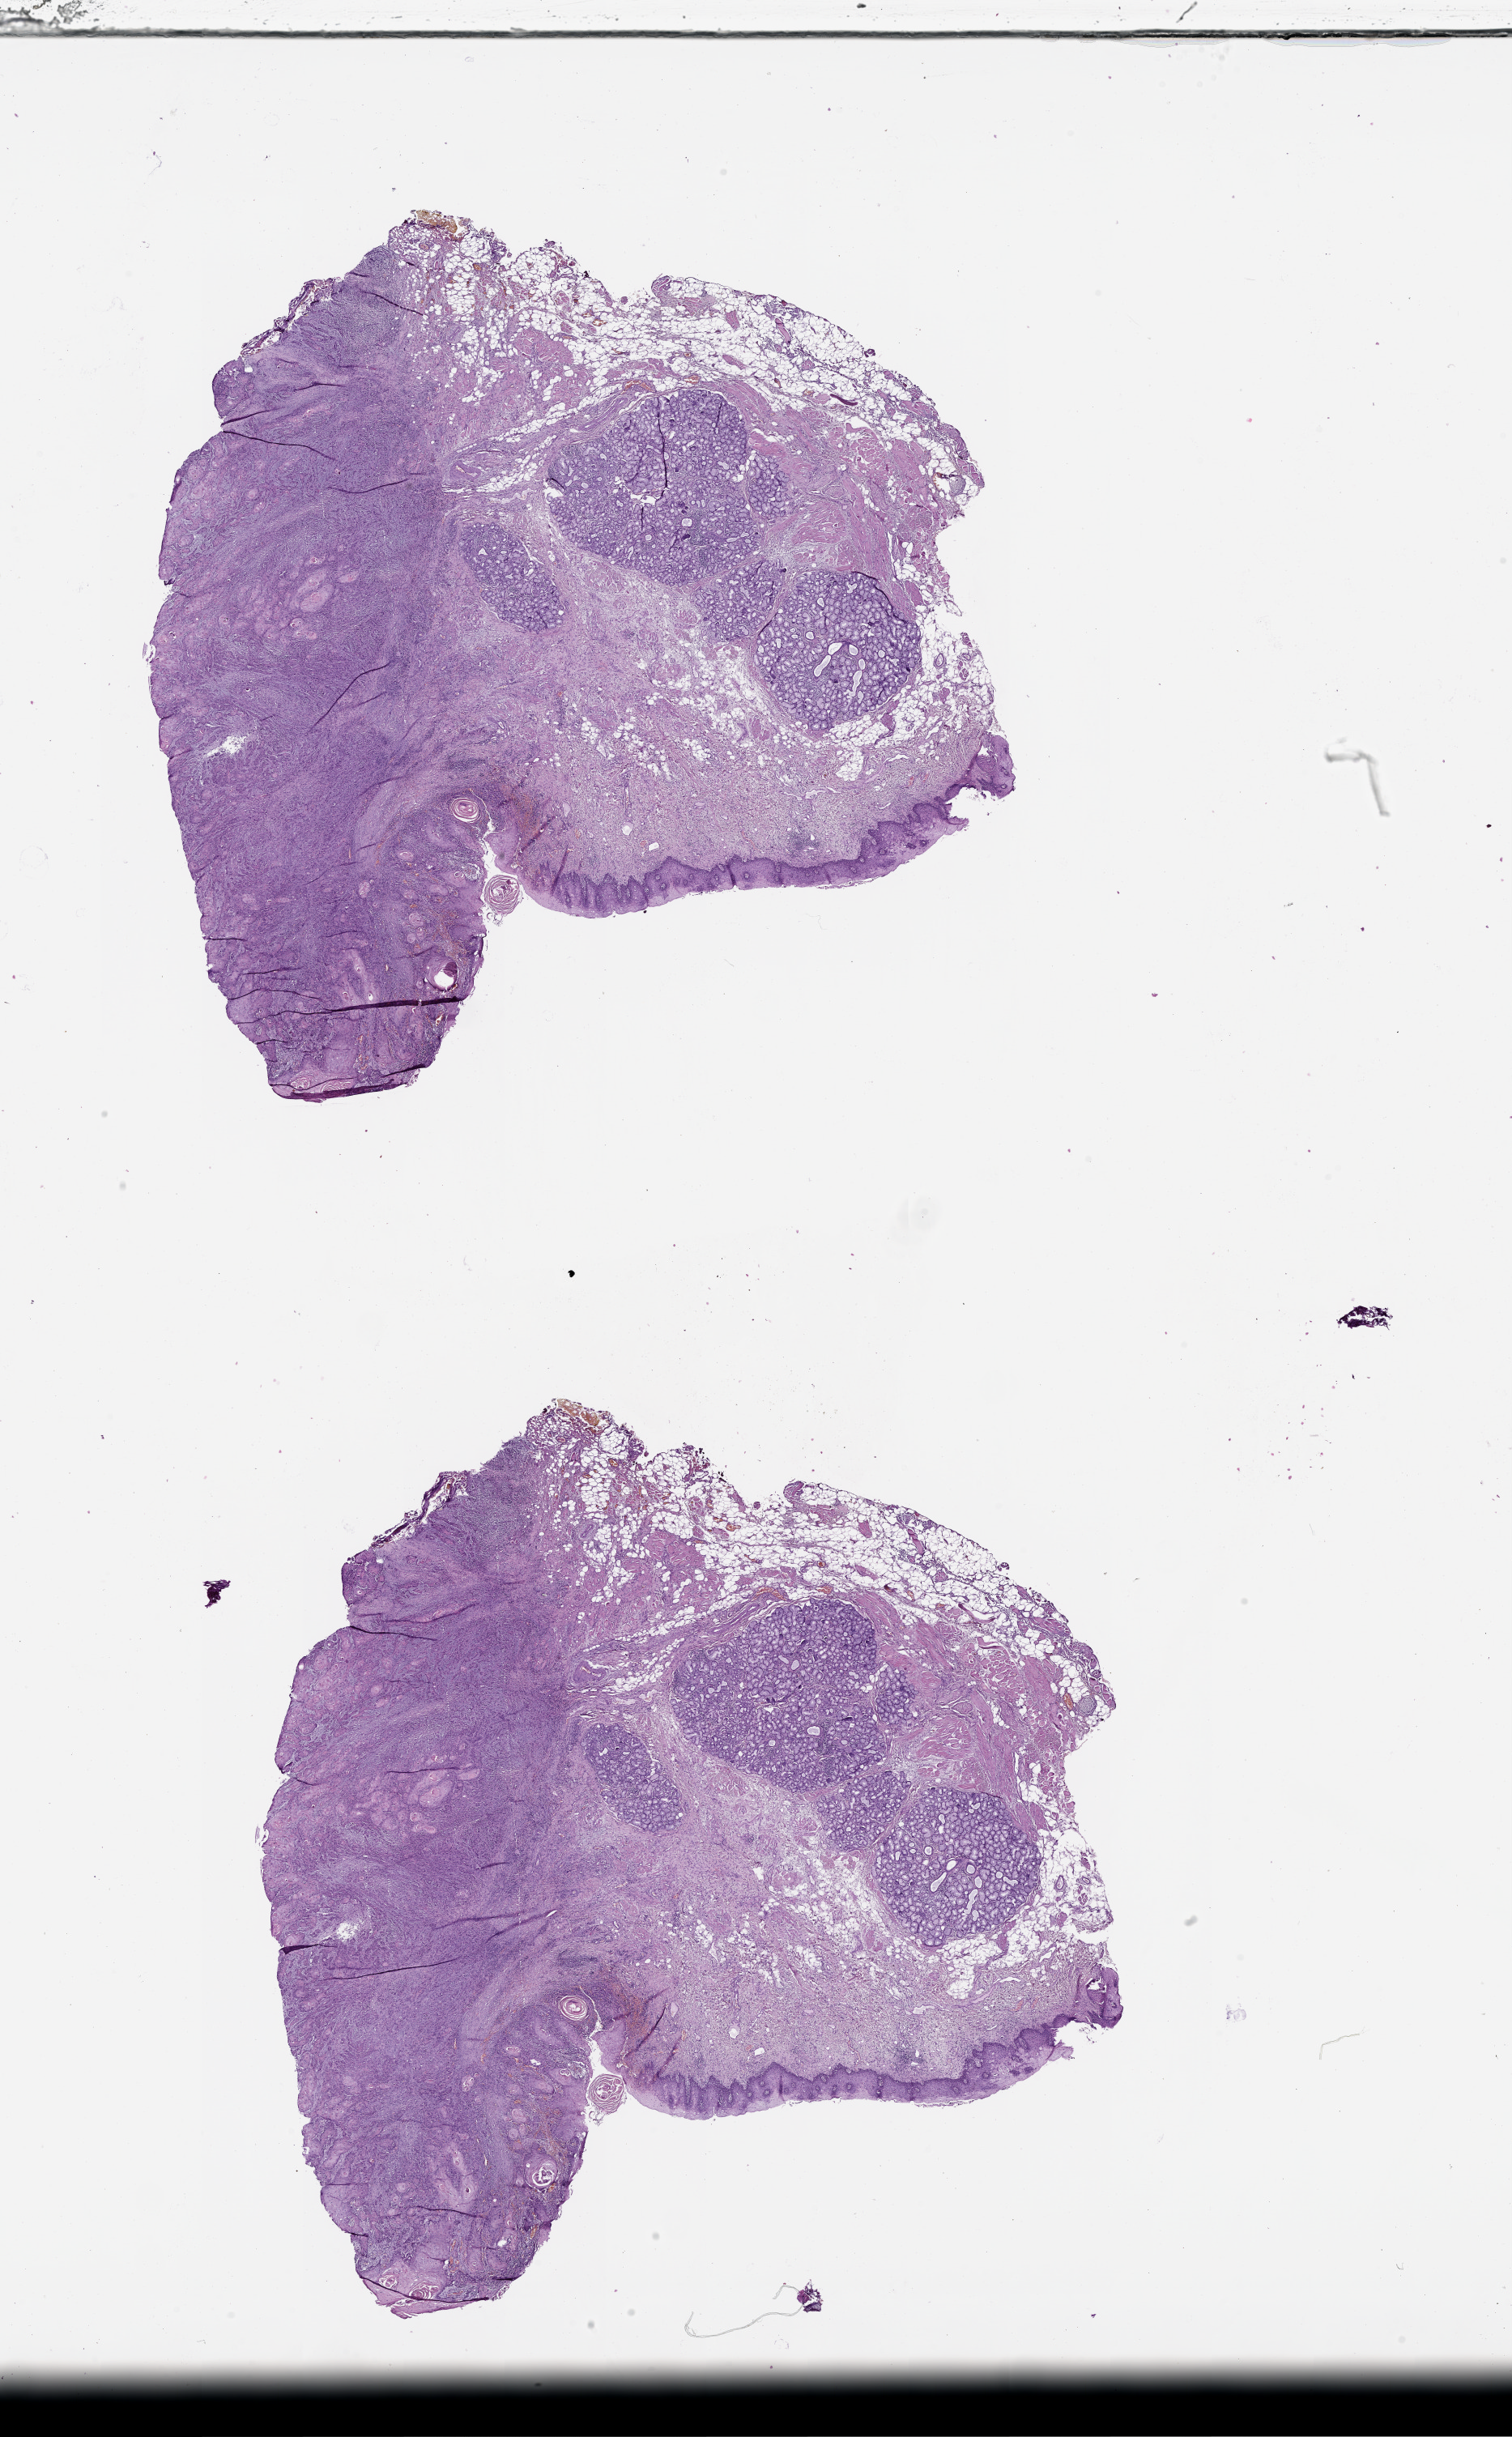
Digitized H&E tissue section (whole slide) — low-resolution overview of the scanned area, about 15.0 x 24.2 mm, head and neck, tissue type not recorded.
- patient diagnosis (cohort enrolment): head and neck cancer (head-neck)